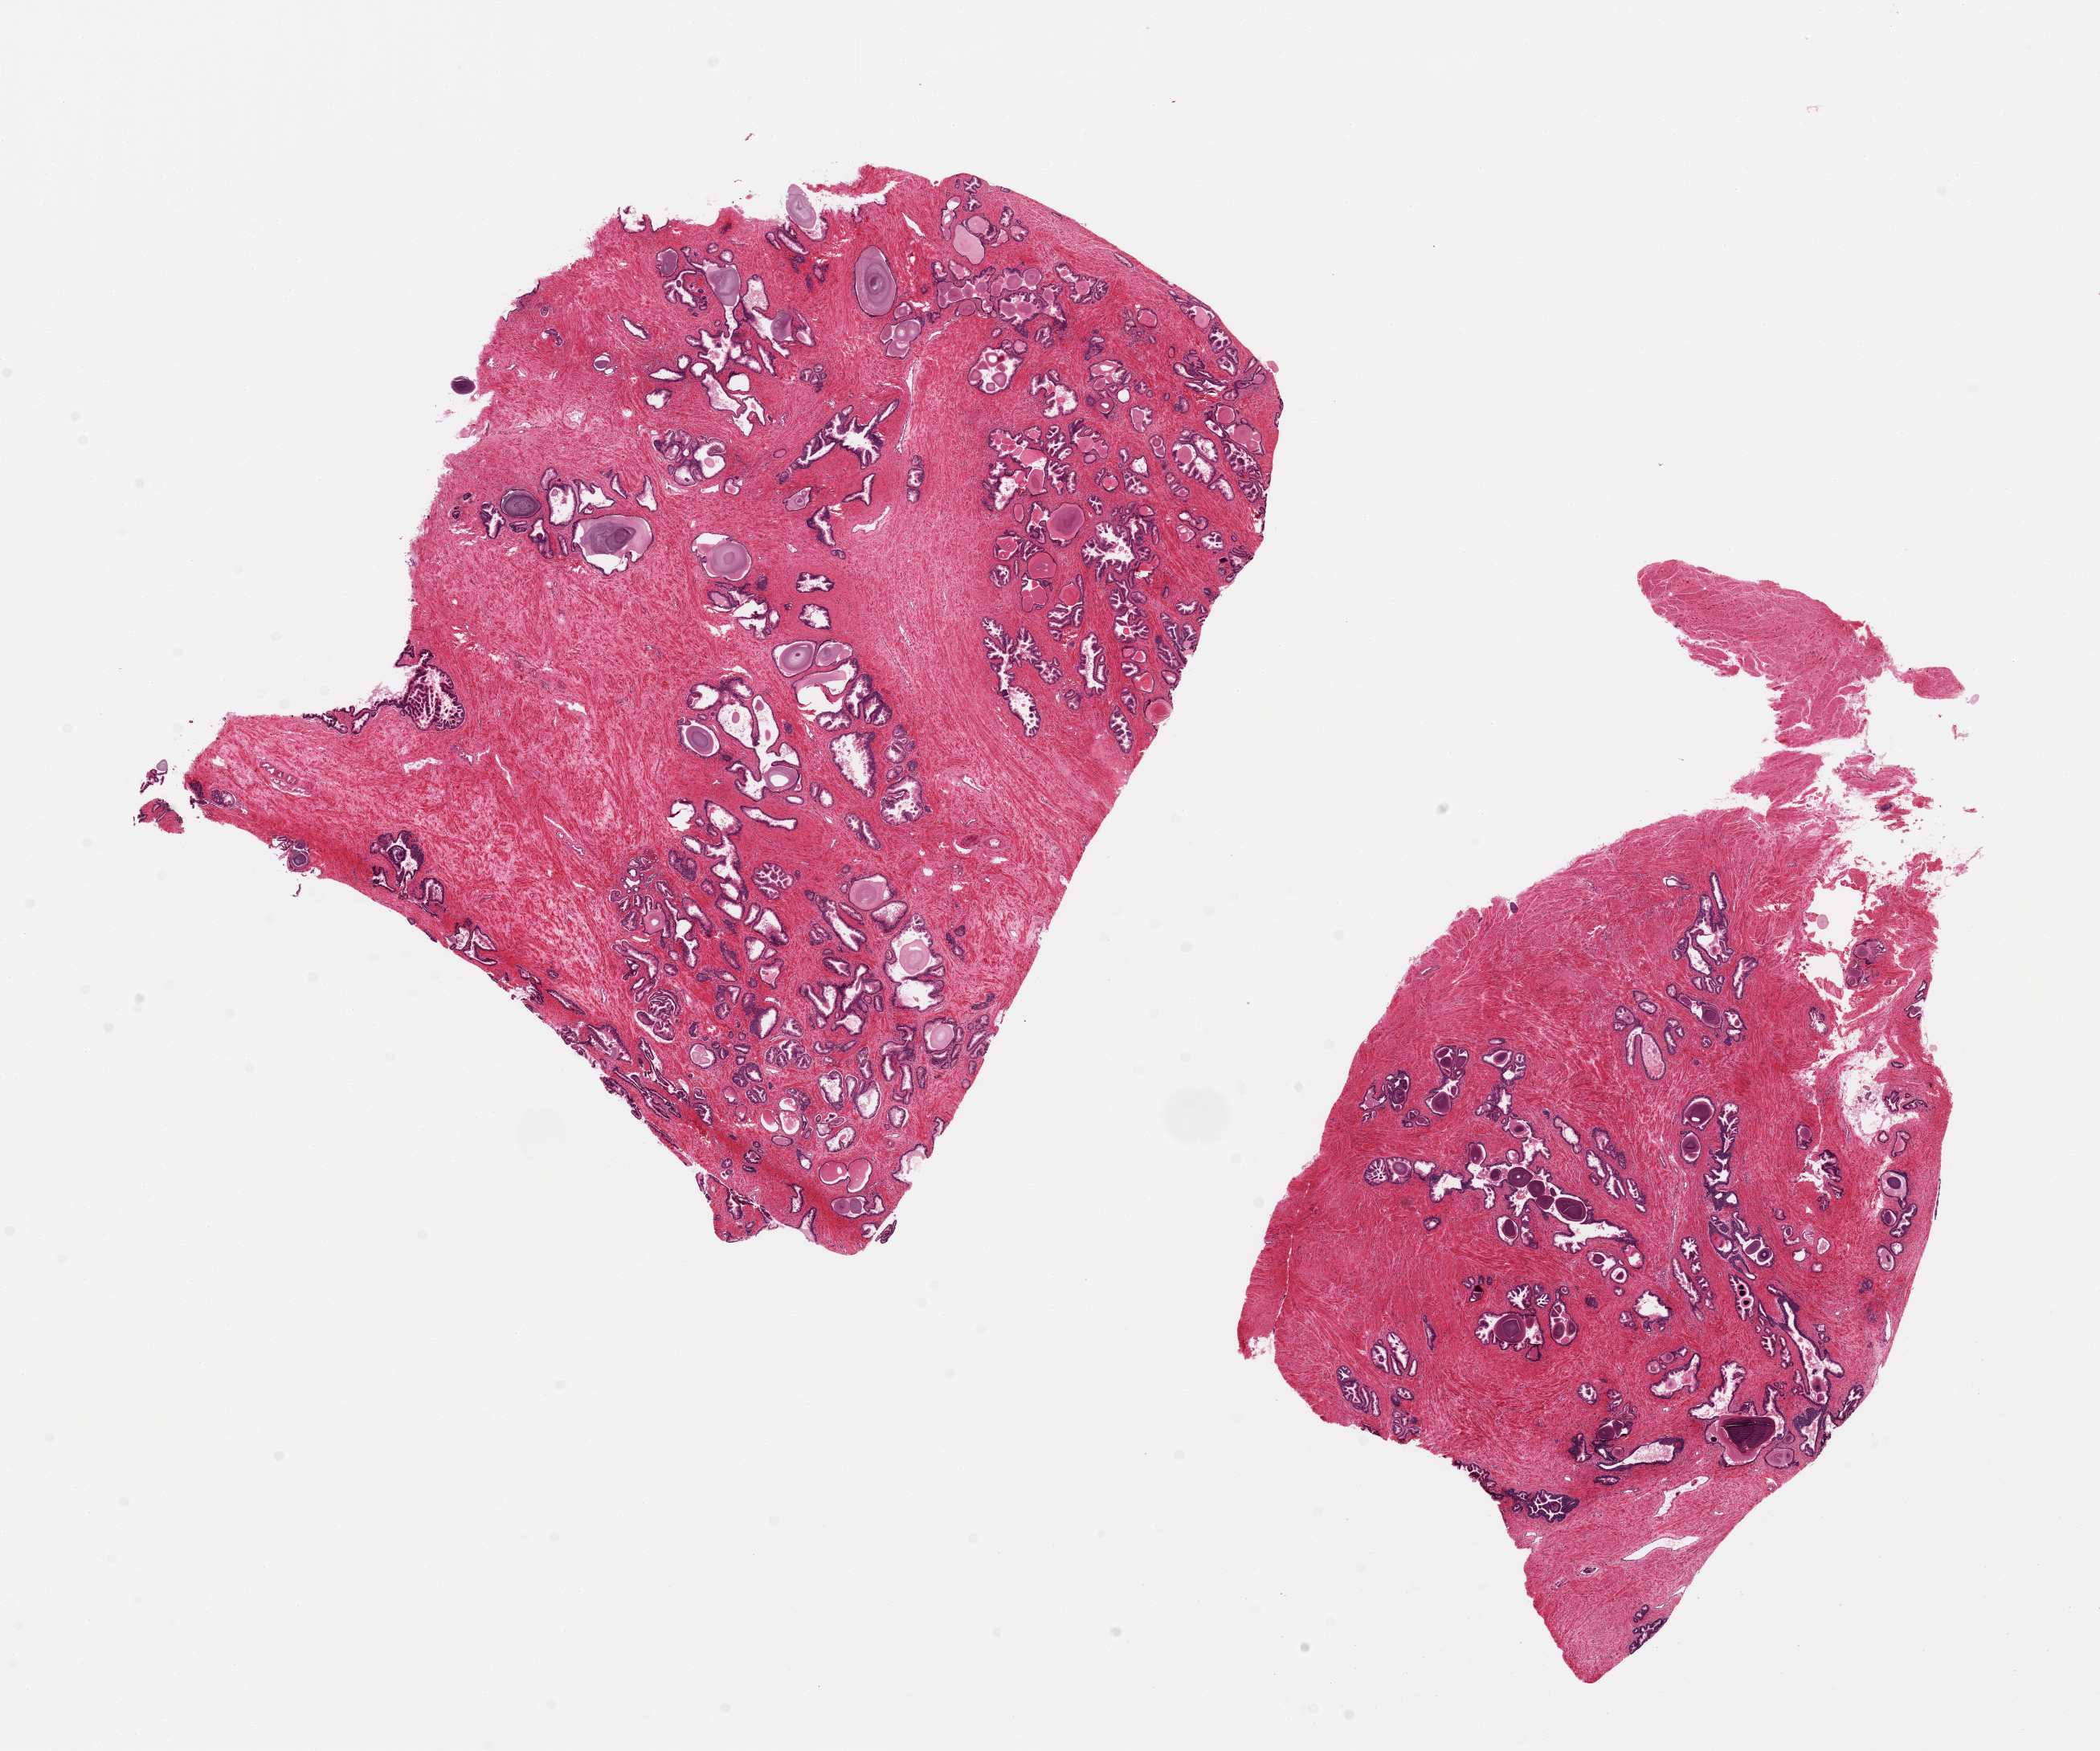
Digitized H&E-stained section — whole scanned area (about 20.7 x 17.2 mm) shown as a low-resolution overview, PAXgene-fixed paraffin-embedded (PFPE) section, sampled site (target tissue): prostate, tissue donor sample.
Review note (as recorded): 2 ~9x6.5mm aliquots, patchy glandular/stroma hyperplasia.